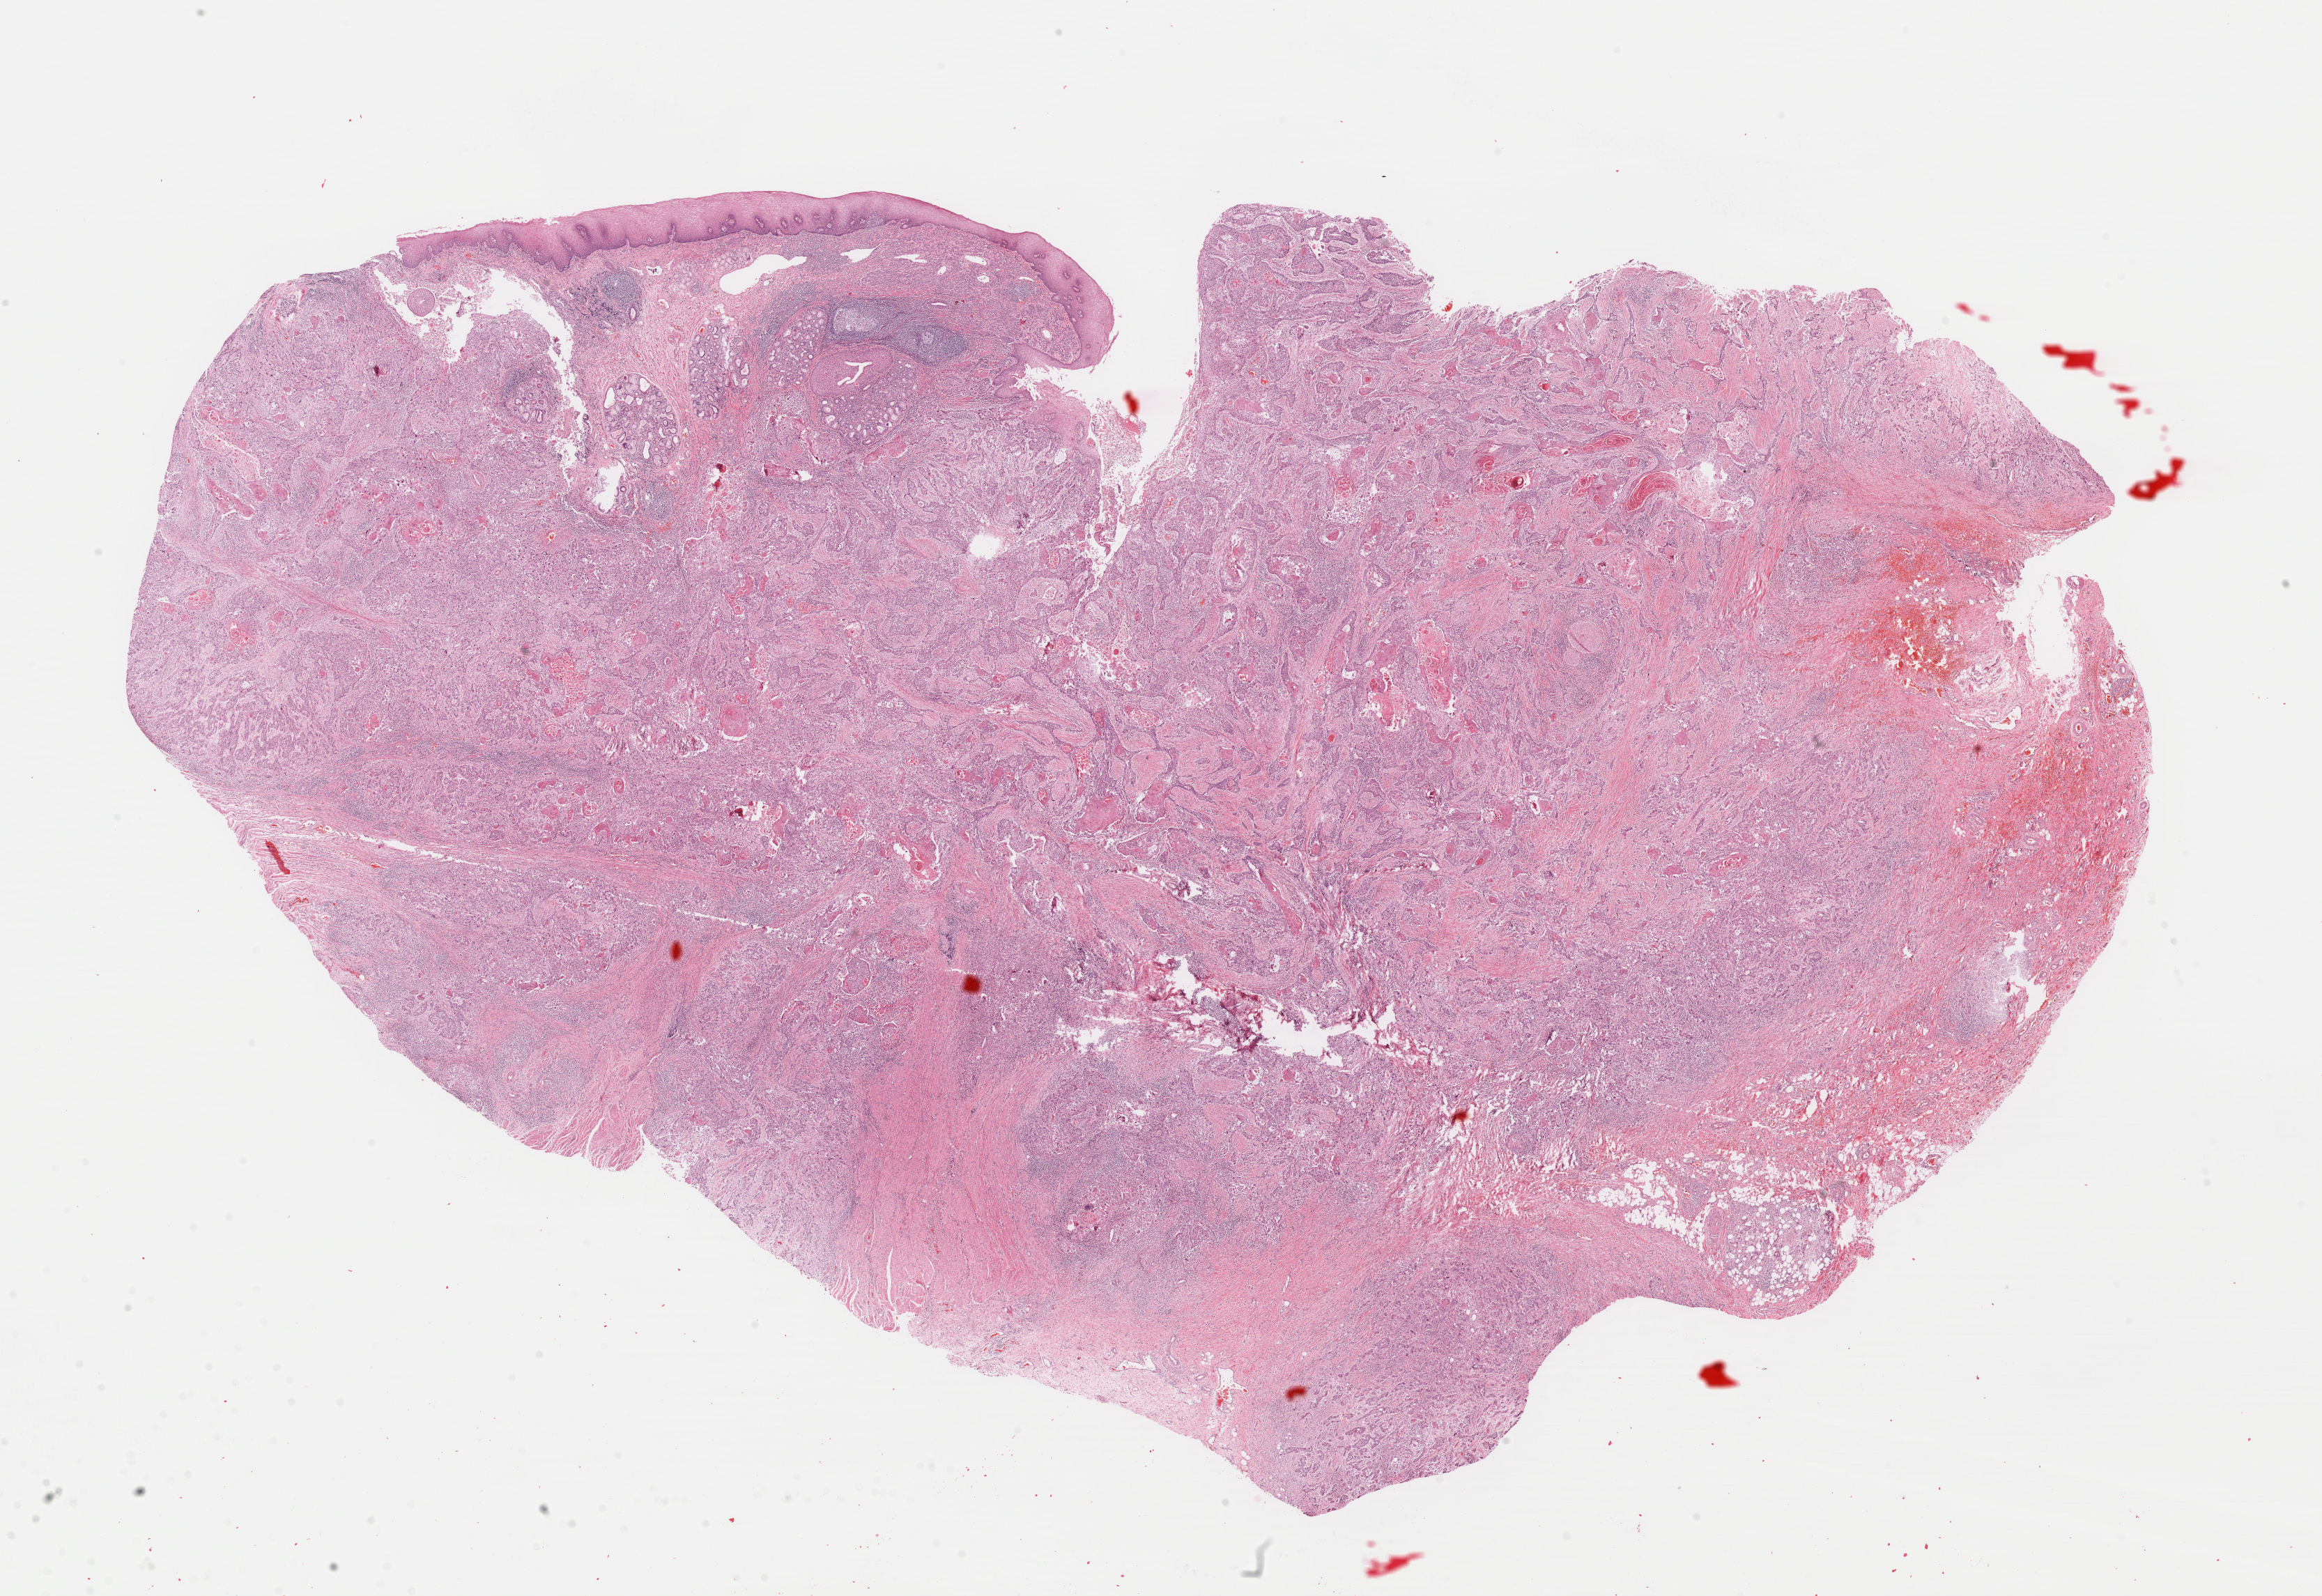
H&E-stained whole-slide image, shown as a low-resolution overview of the whole scanned area (about 26.3 x 18.1 mm, slide scanned at 40x), formalin-fixed paraffin-embedded (FFPE) diagnostic section, primary tumour sample from the esophagus. Male, age 62 years at initial diagnosis. Histologic grade: G2 (moderately differentiated).
AJCC pathologic stage: IIIA. Pathologic diagnosis: Squamous cell carcinoma, NOS (lower third of esophagus). Lymph nodes positive (case pathology): 1 of 5 examined.